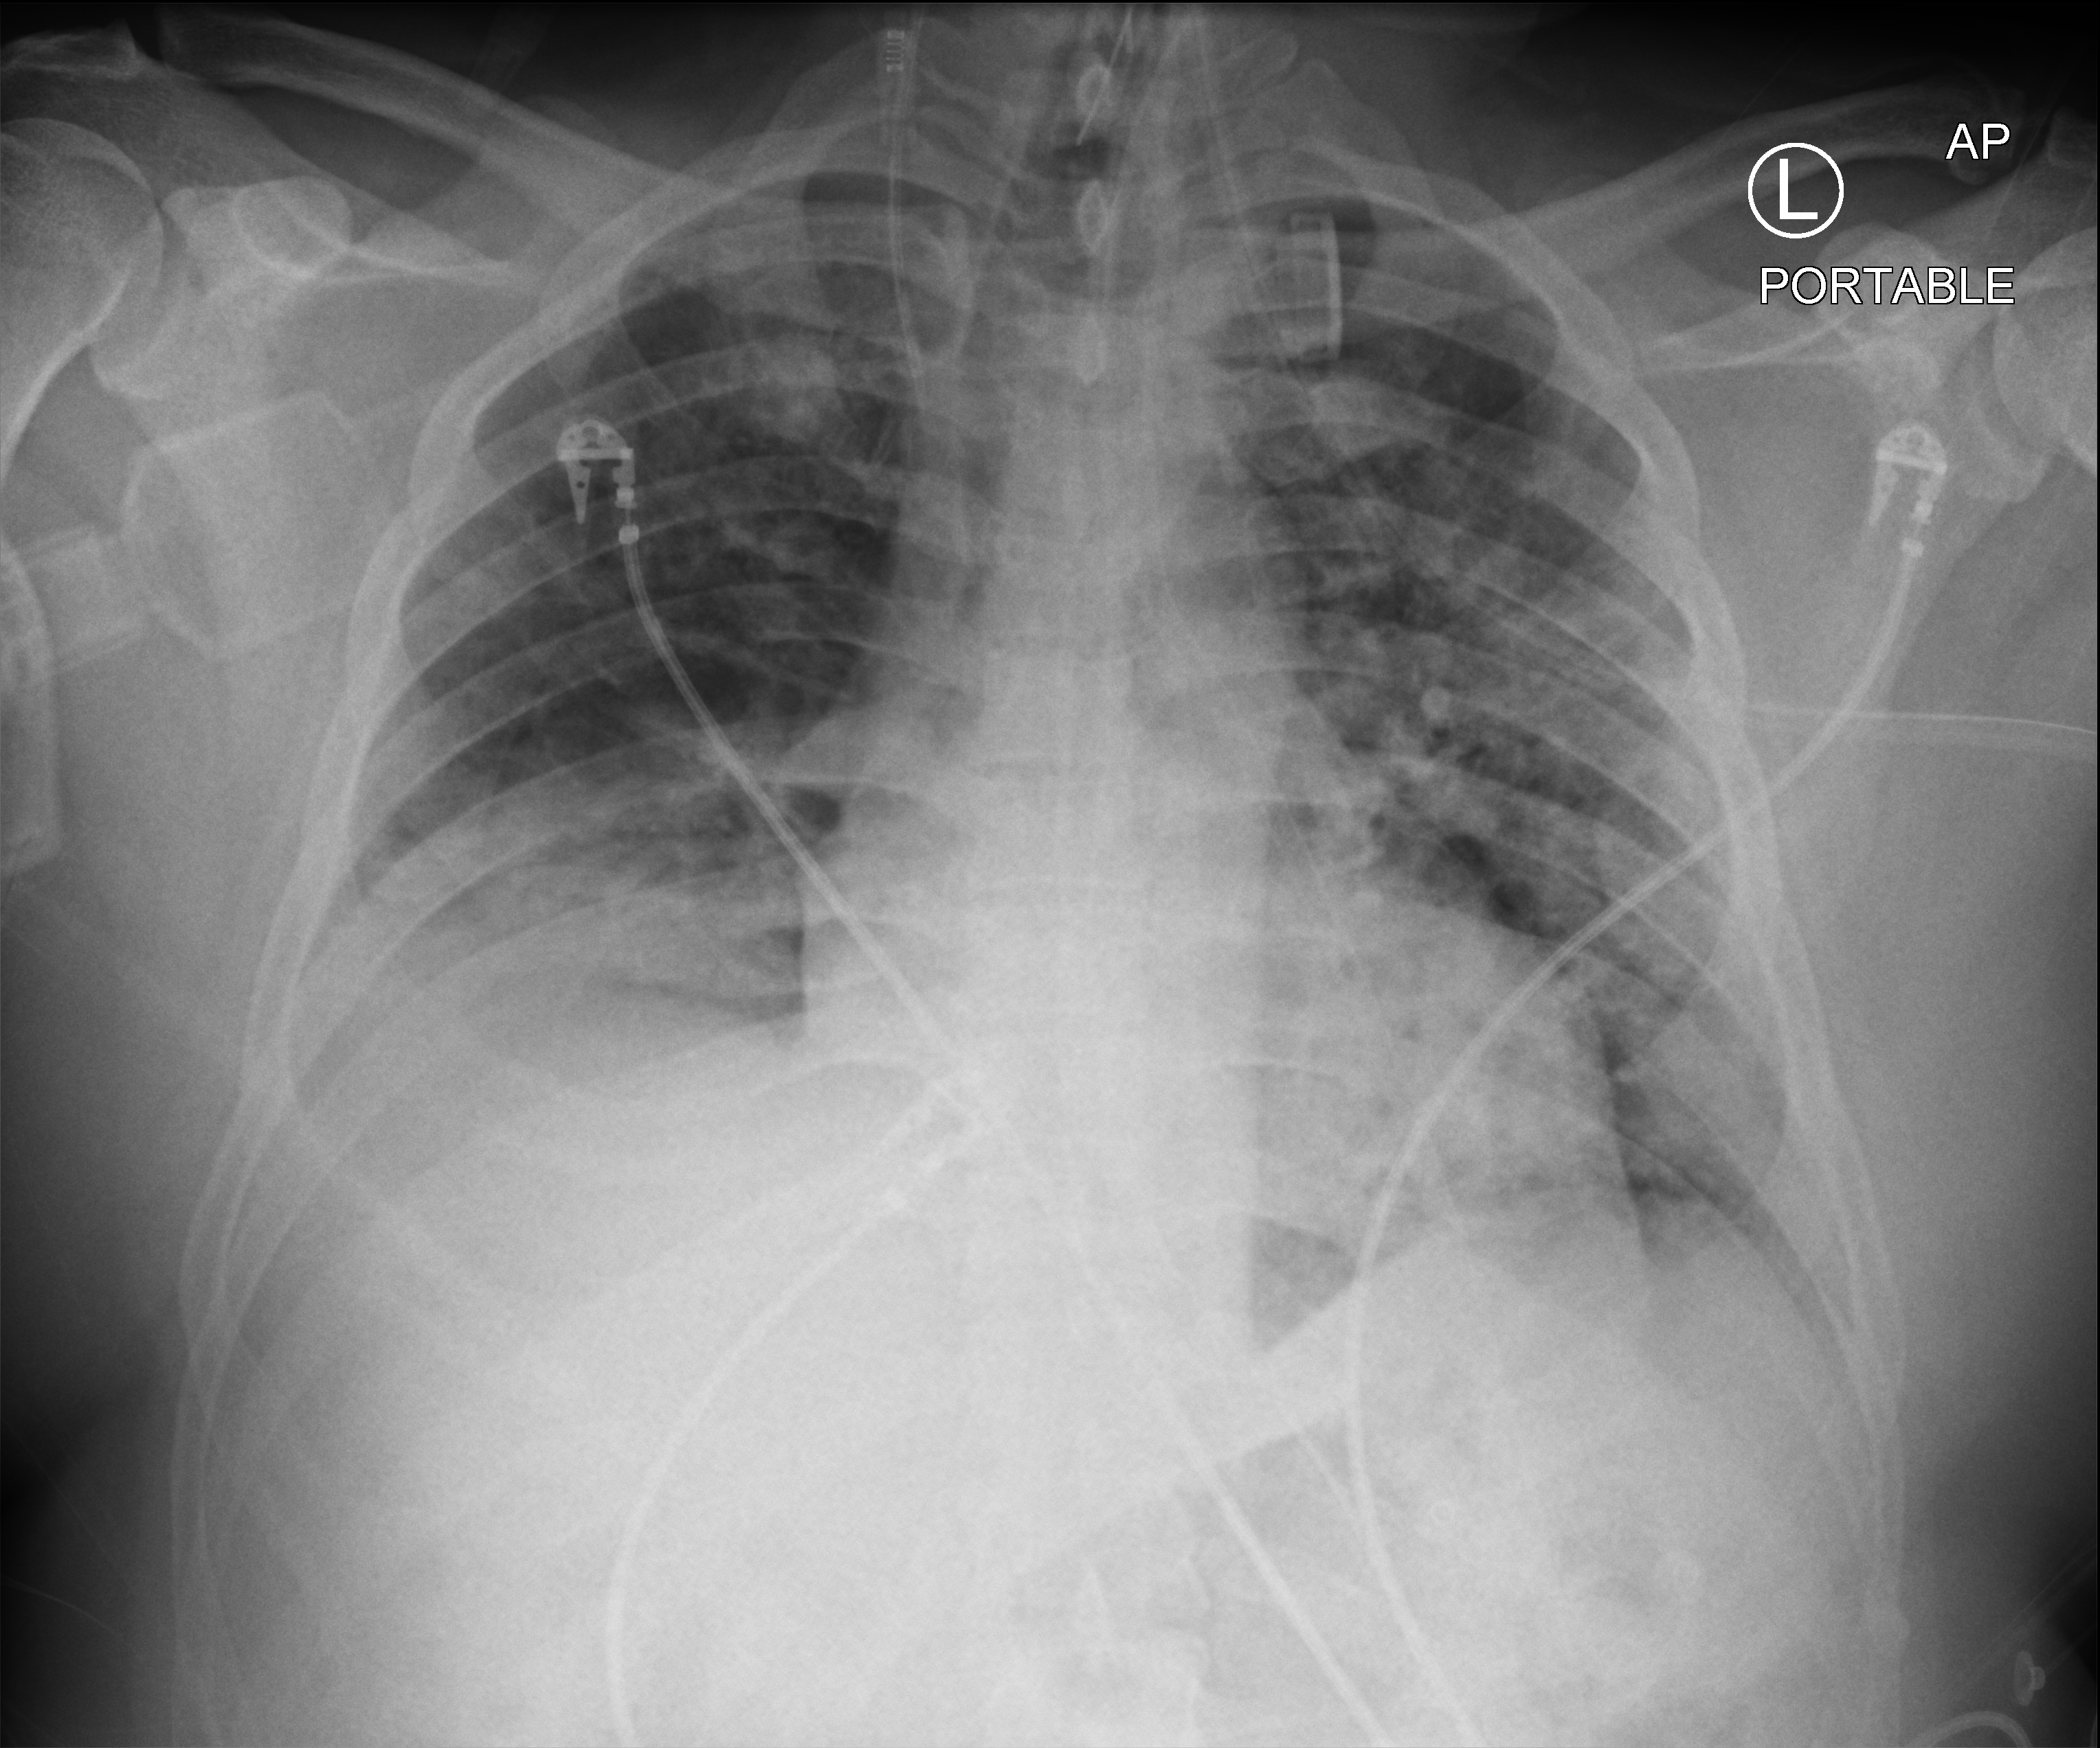
Bedside chest radiograph (computed radiography), anteroposterior (AP) projection. Patient hospitalised with COVID-19; male, aged 18–59 years.
Admission-level facts for this patient (not findings on this image; timing relative to this image not recorded):
- length of hospital stay: 29 days